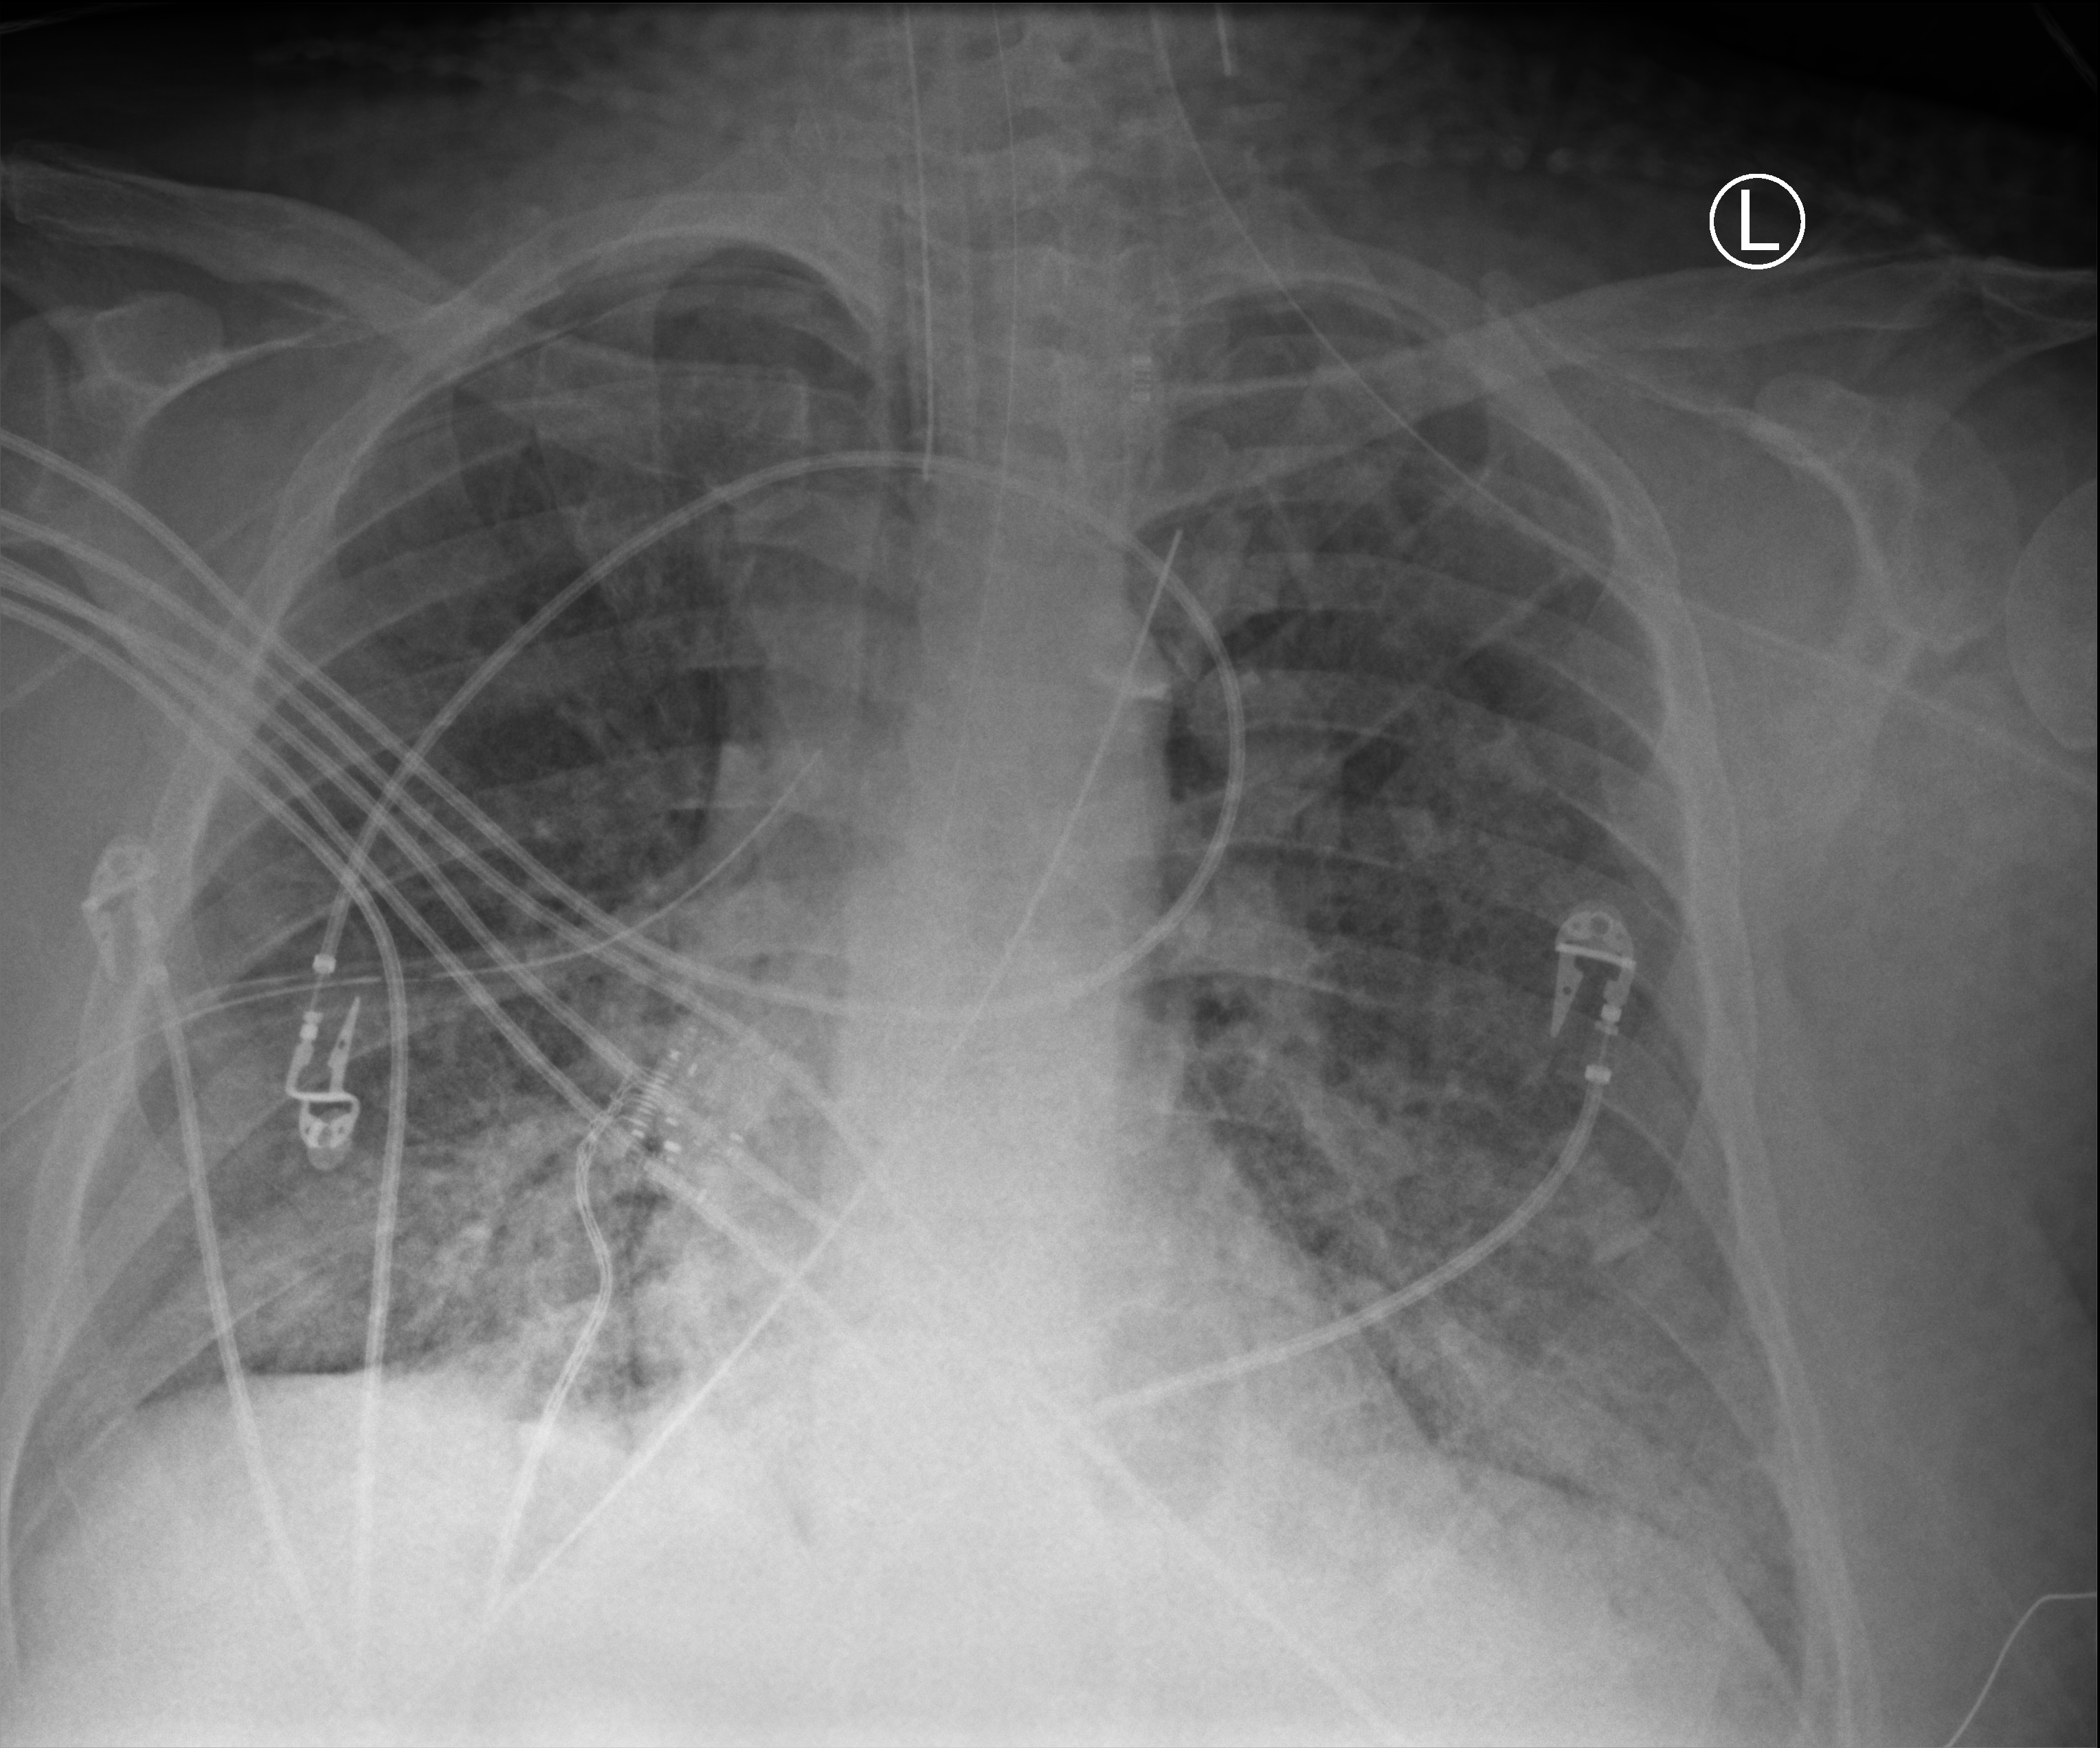
Bedside chest radiograph (computed radiography). Adult patient hospitalised with COVID-19, age 18–59 years.
Admission-level facts for this patient (not findings on this image; timing relative to this image not recorded): length of hospital stay: 26 days; hypertension (admission record): yes.